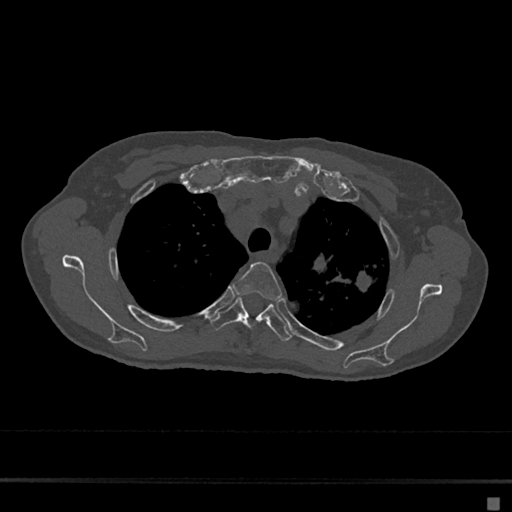
CT including the spine, one axial slice; slice 519 of 797 in the series (ordered by position); reconstruction kernel Br40s/3; 120 kVp; bone window (W 1800 / L 400 HU); 0.5 mm slice thickness; 512 × 512 image matrix, field of view 360 × 360 mm. Female patient, age 68 years. From the clinical record (not read from this slice): primary cancer: renal.
Annotated regions visible in this slice (semi-automatic segmentation, software-assisted and operator-edited):
- T3 vertebra: box from (x=231, y=262) to (x=282, y=300) px
- T4 vertebra: (x=210, y=298)–(x=291, y=342)